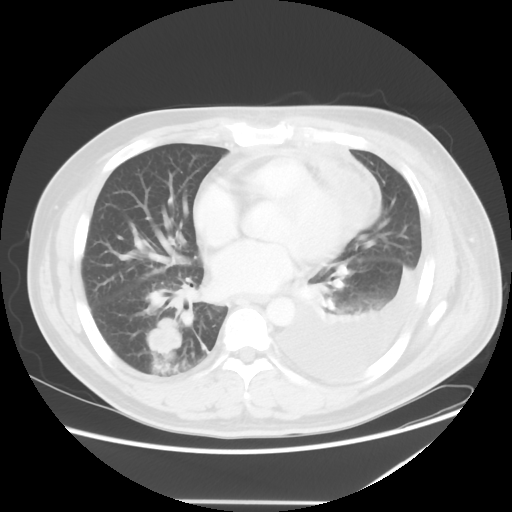
Chest CT, one axial slice; slice 23 of 52 in the series (ordered by position); reconstruction kernel STANDARD; lung window (W 1500 / L -600 HU); 5 mm slice thickness; 512 × 512 image matrix, field of view 405 × 405 mm. Patient: male, 42 years. Case-level facts recorded for this patient, not image findings: clinical TNM (as recorded): T2 N1 M1.
Outlined on this slice (bounding box drawn by a radiologist):
- lung tumour (recorded histology: adenocarcinoma): bounding box (x1, y1, x2, y2) in pixels: (143, 315, 186, 363)